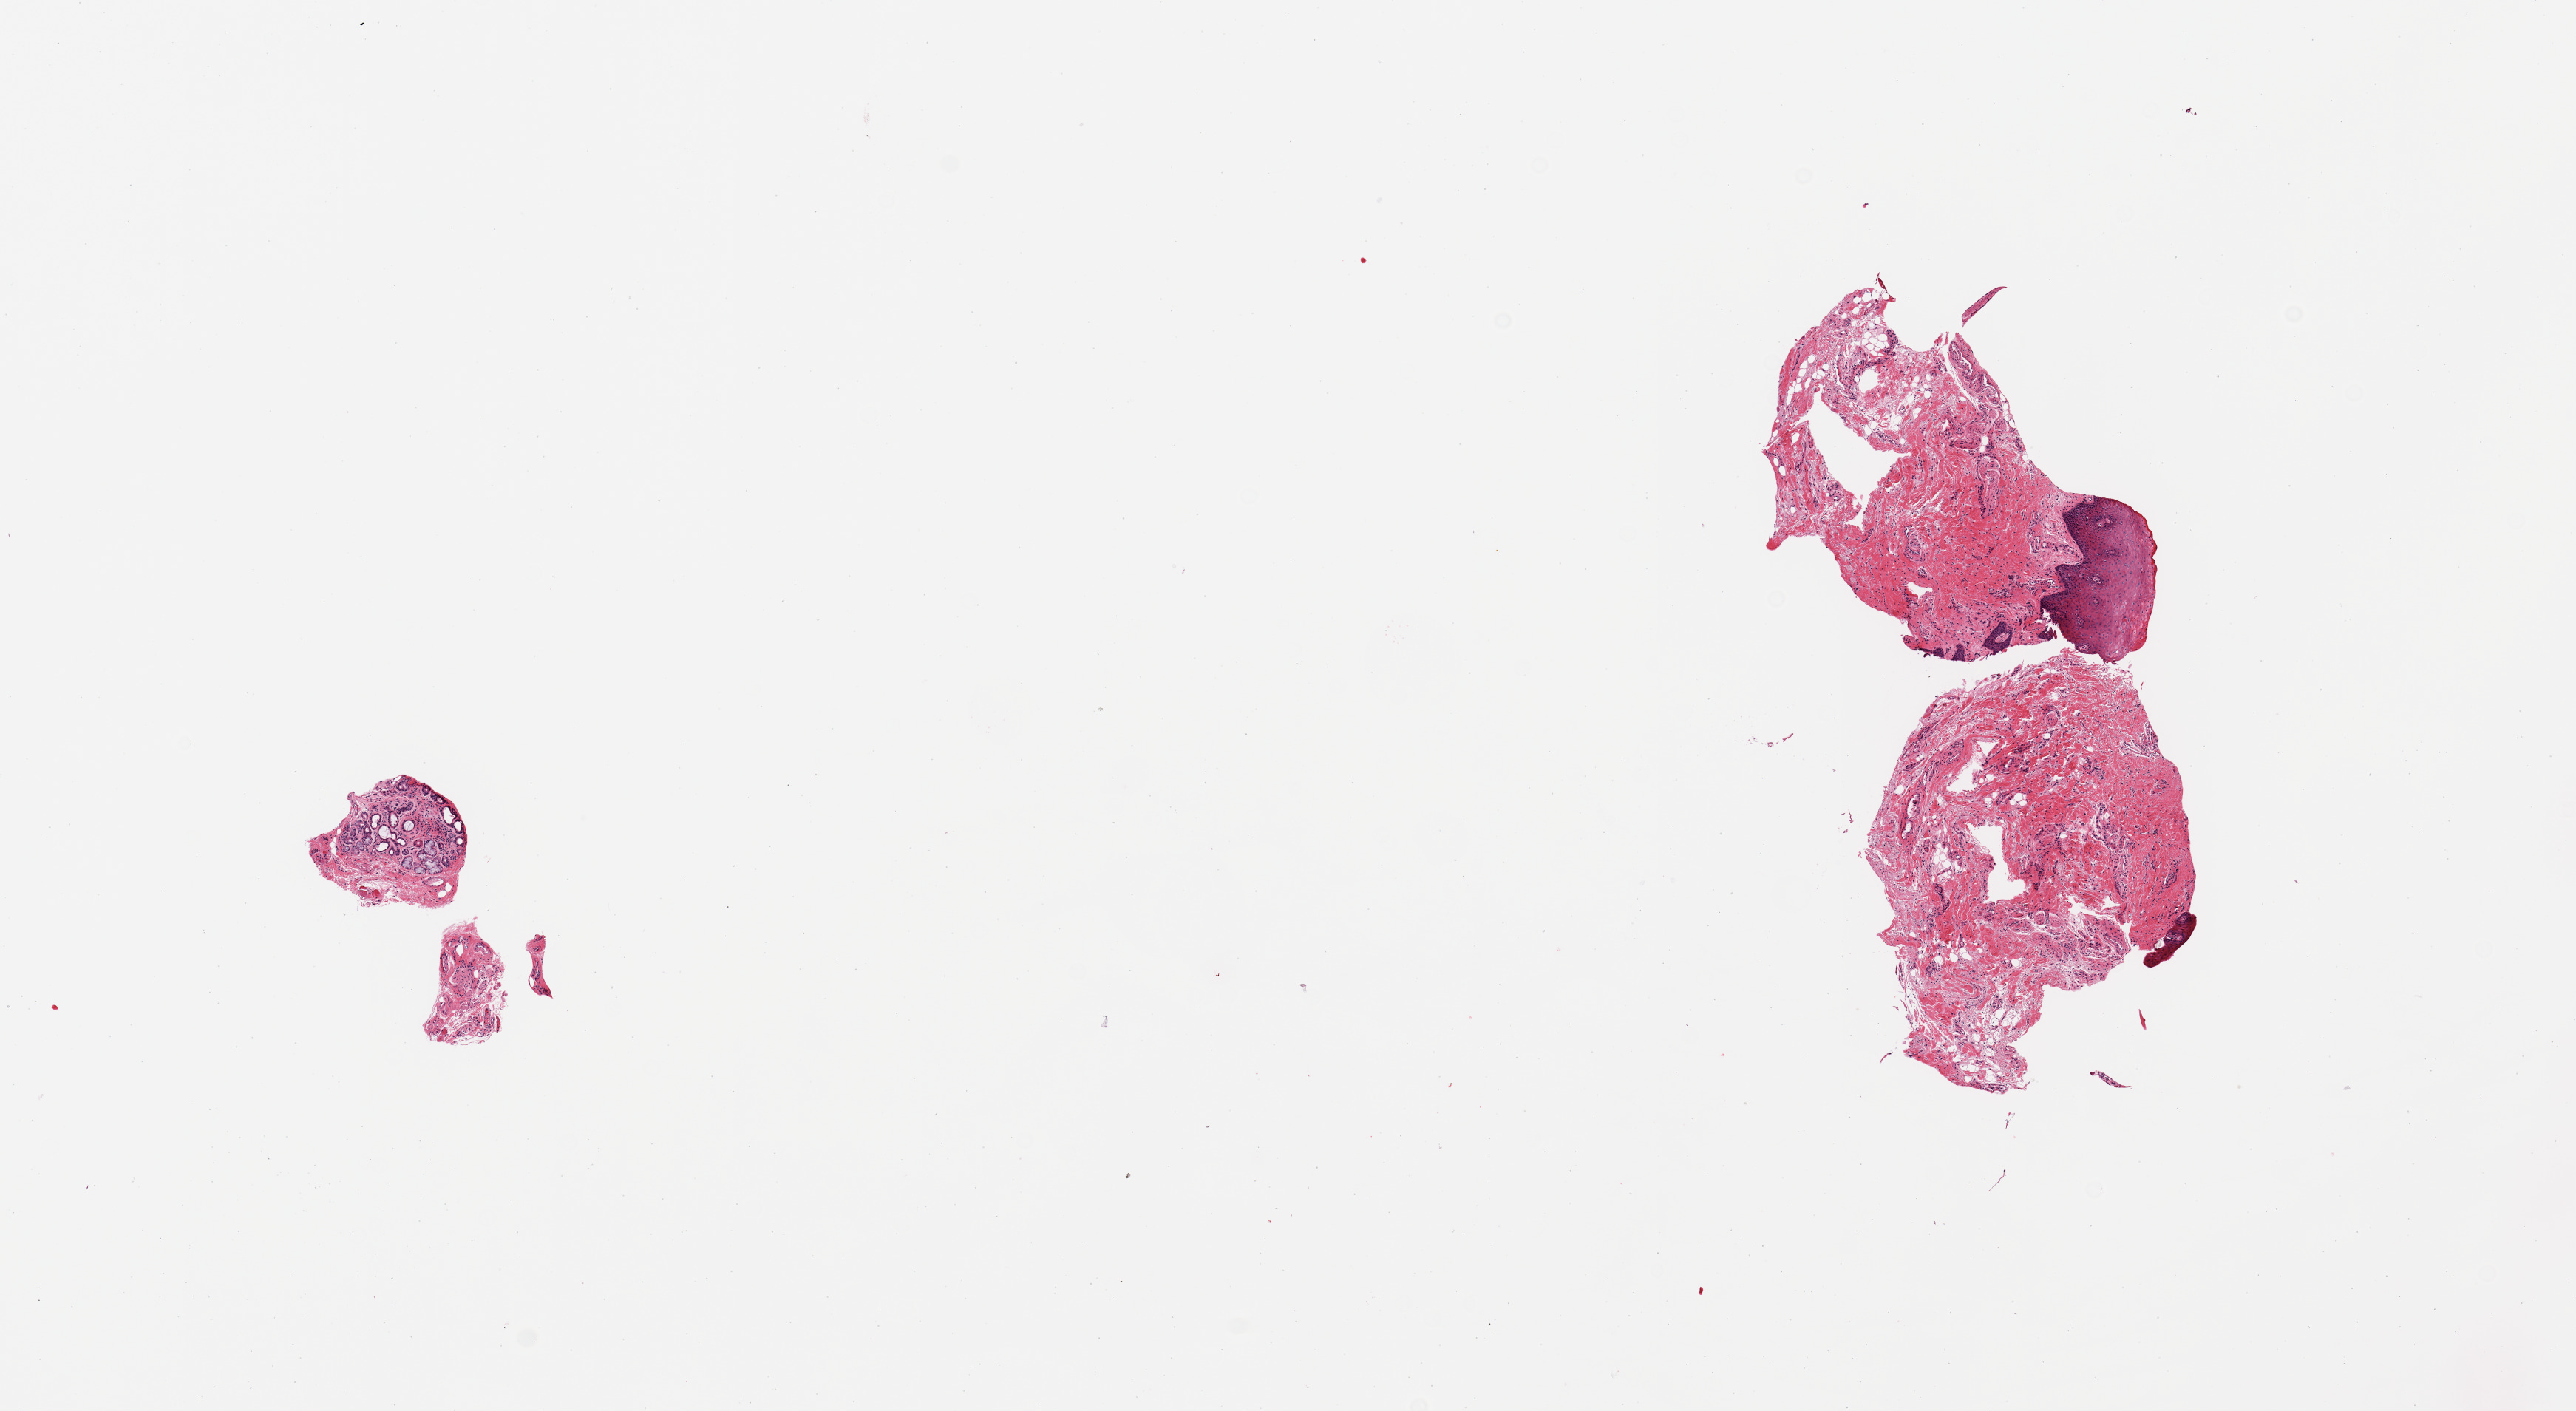
Haematoxylin and eosin whole-slide image, low-resolution overview of the scanned area, about 13.8 x 7.5 mm; PAXgene-fixed paraffin-embedded (PFPE) section; target tissue: minor salivary gland; donor tissue sample. Donor sex: male.
Pathologist's review note for this sample: 2 pieces; <1mm salivary gland; remainder is lip and connective tissue.